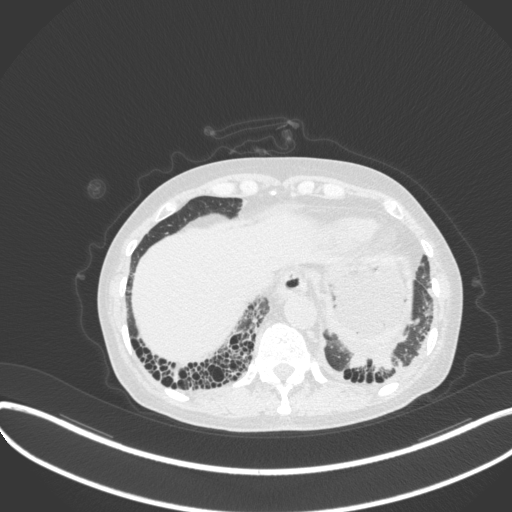
Chest CT, one axial slice; position 54 of 373 along the scan axis; 120 kVp; lung window (W 1500 / L -600 HU); 512 × 512 image matrix, field of view 400 × 400 mm. Patient: female, 56 years. Case-level facts recorded for this patient, not image findings: clinical TNM (as recorded): T1 N0 M0.
Structures marked on this image (bounding box drawn by a radiologist):
- lung tumour (recorded histology: adenocarcinoma): bounding box <344,346,401,379> (left, top, right, bottom; pixels)